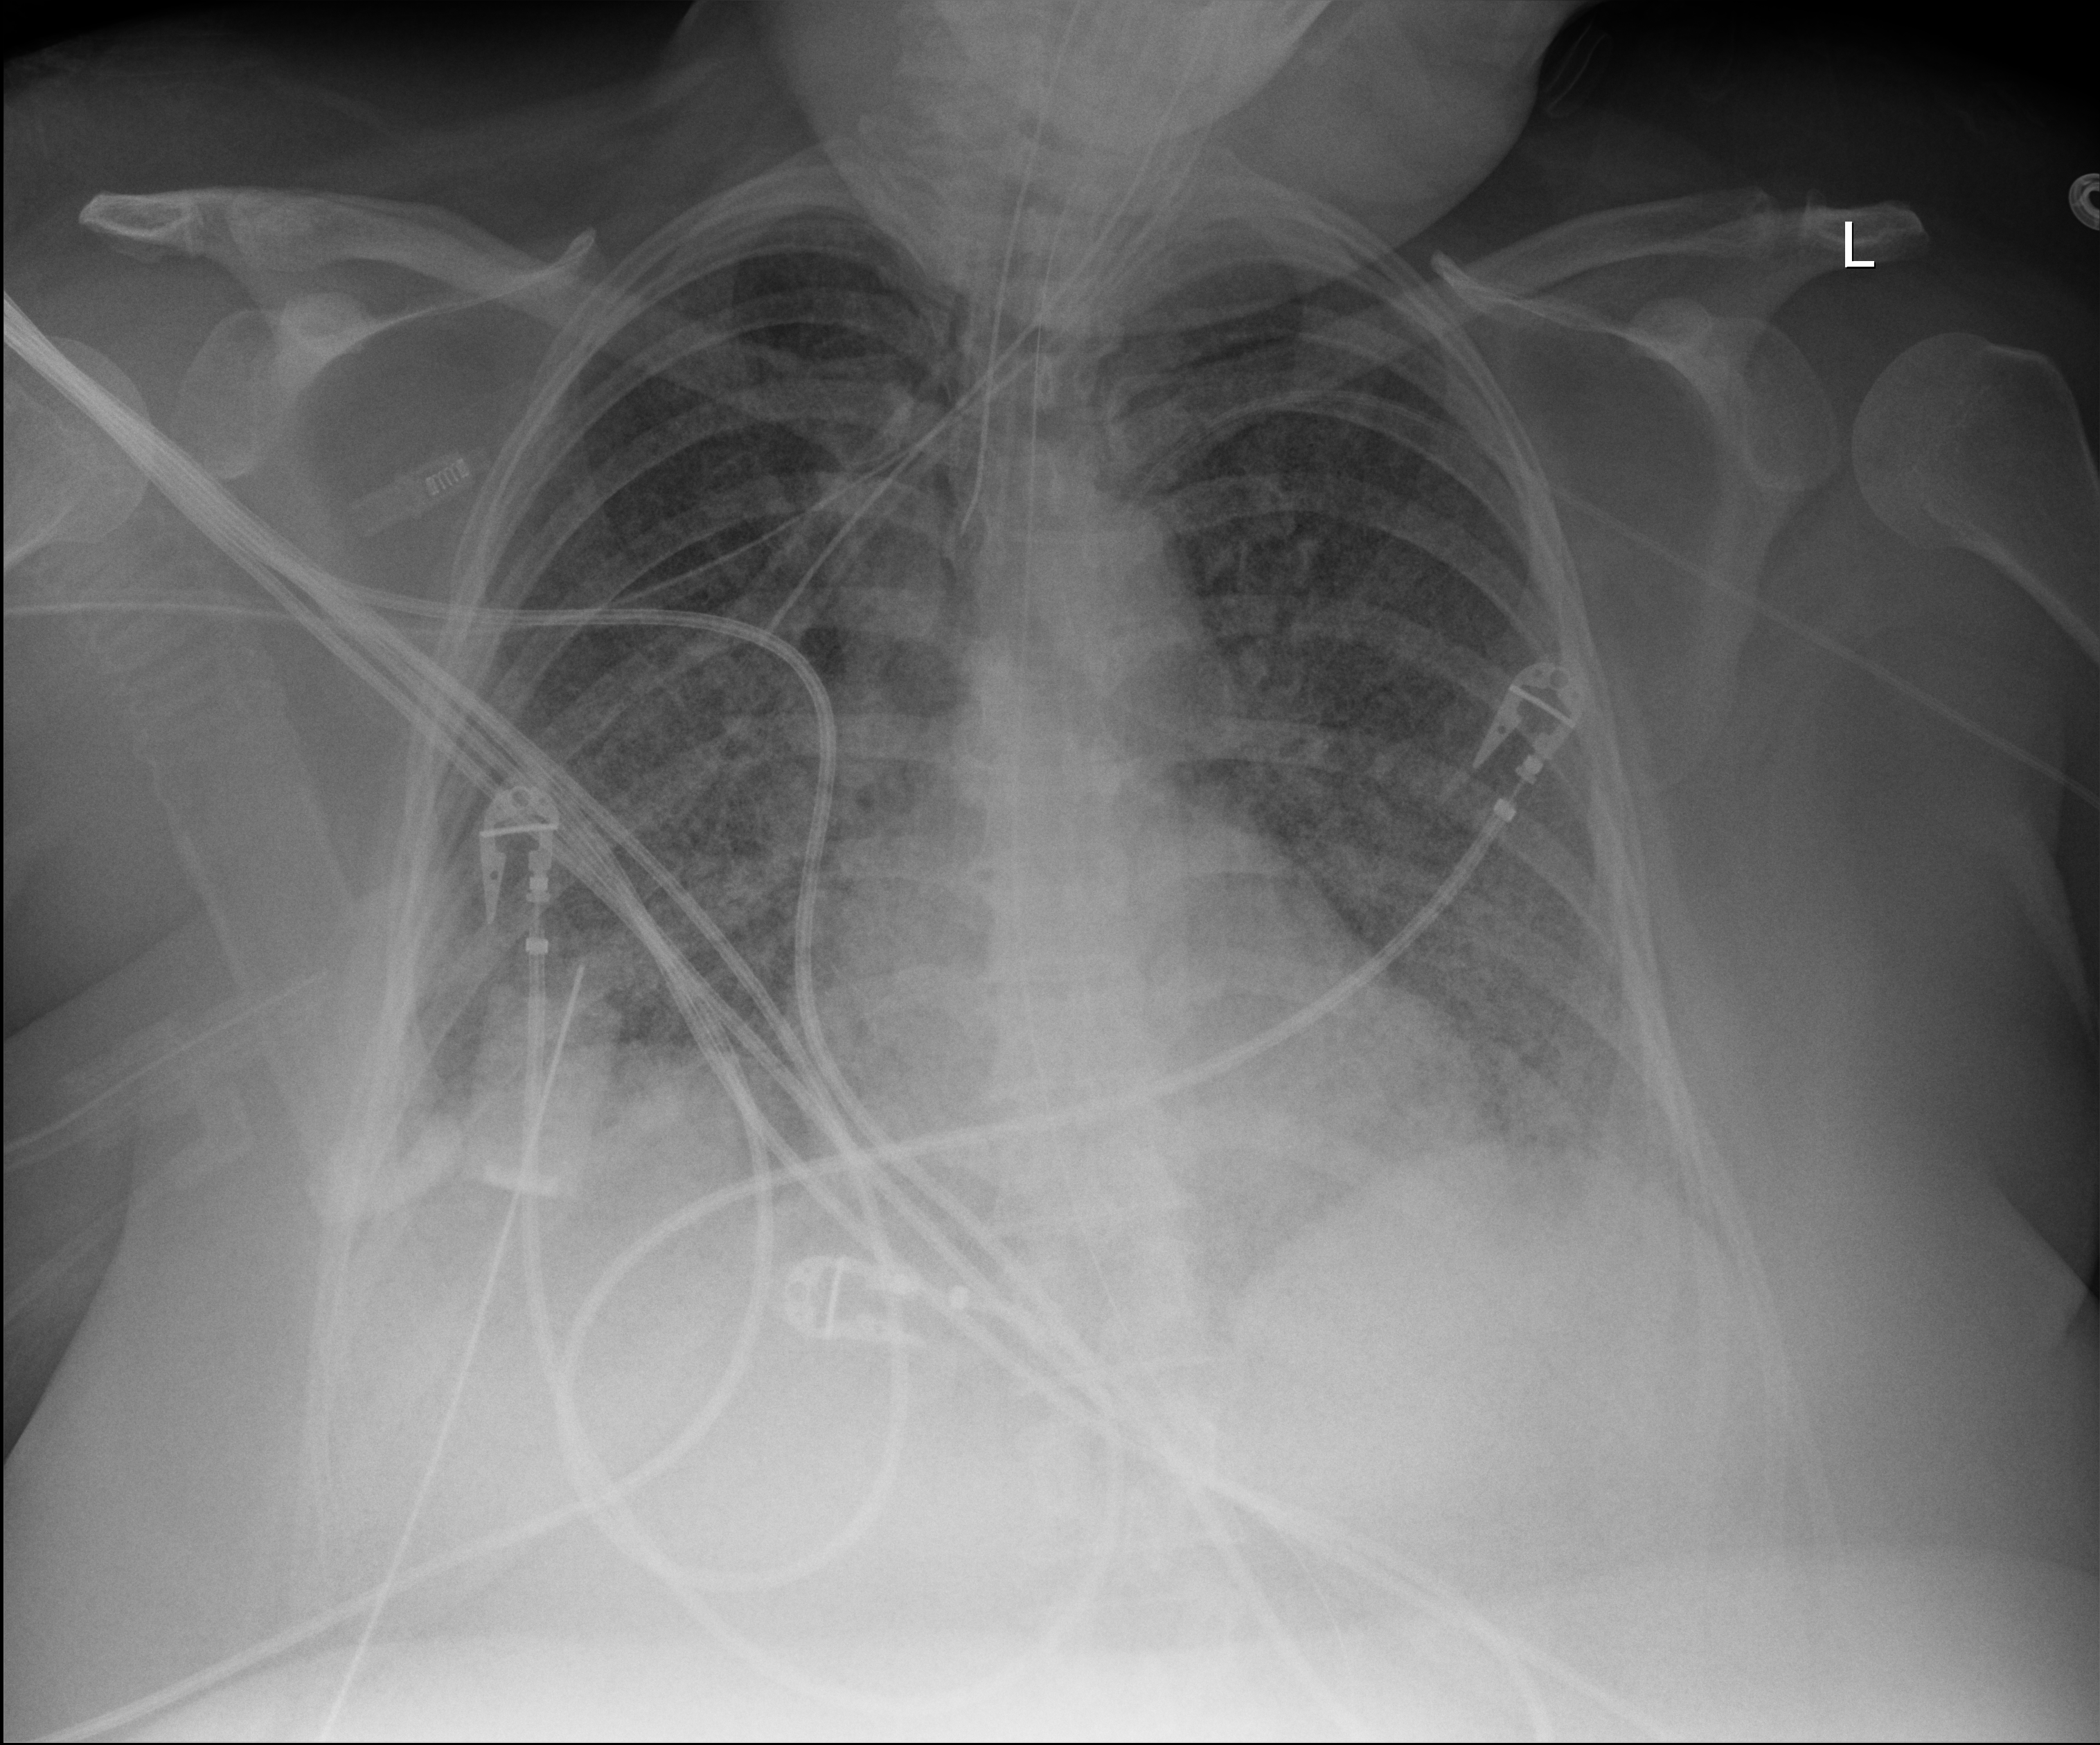
Chest X-ray (portable), anteroposterior (AP) projection. Female patient hospitalised with COVID-19, age 18–59 years.
Admission-level facts for this patient (not findings on this image; timing relative to this image not recorded): admitted to intensive care during this hospital stay: yes; mechanically ventilated during this hospital stay: yes.